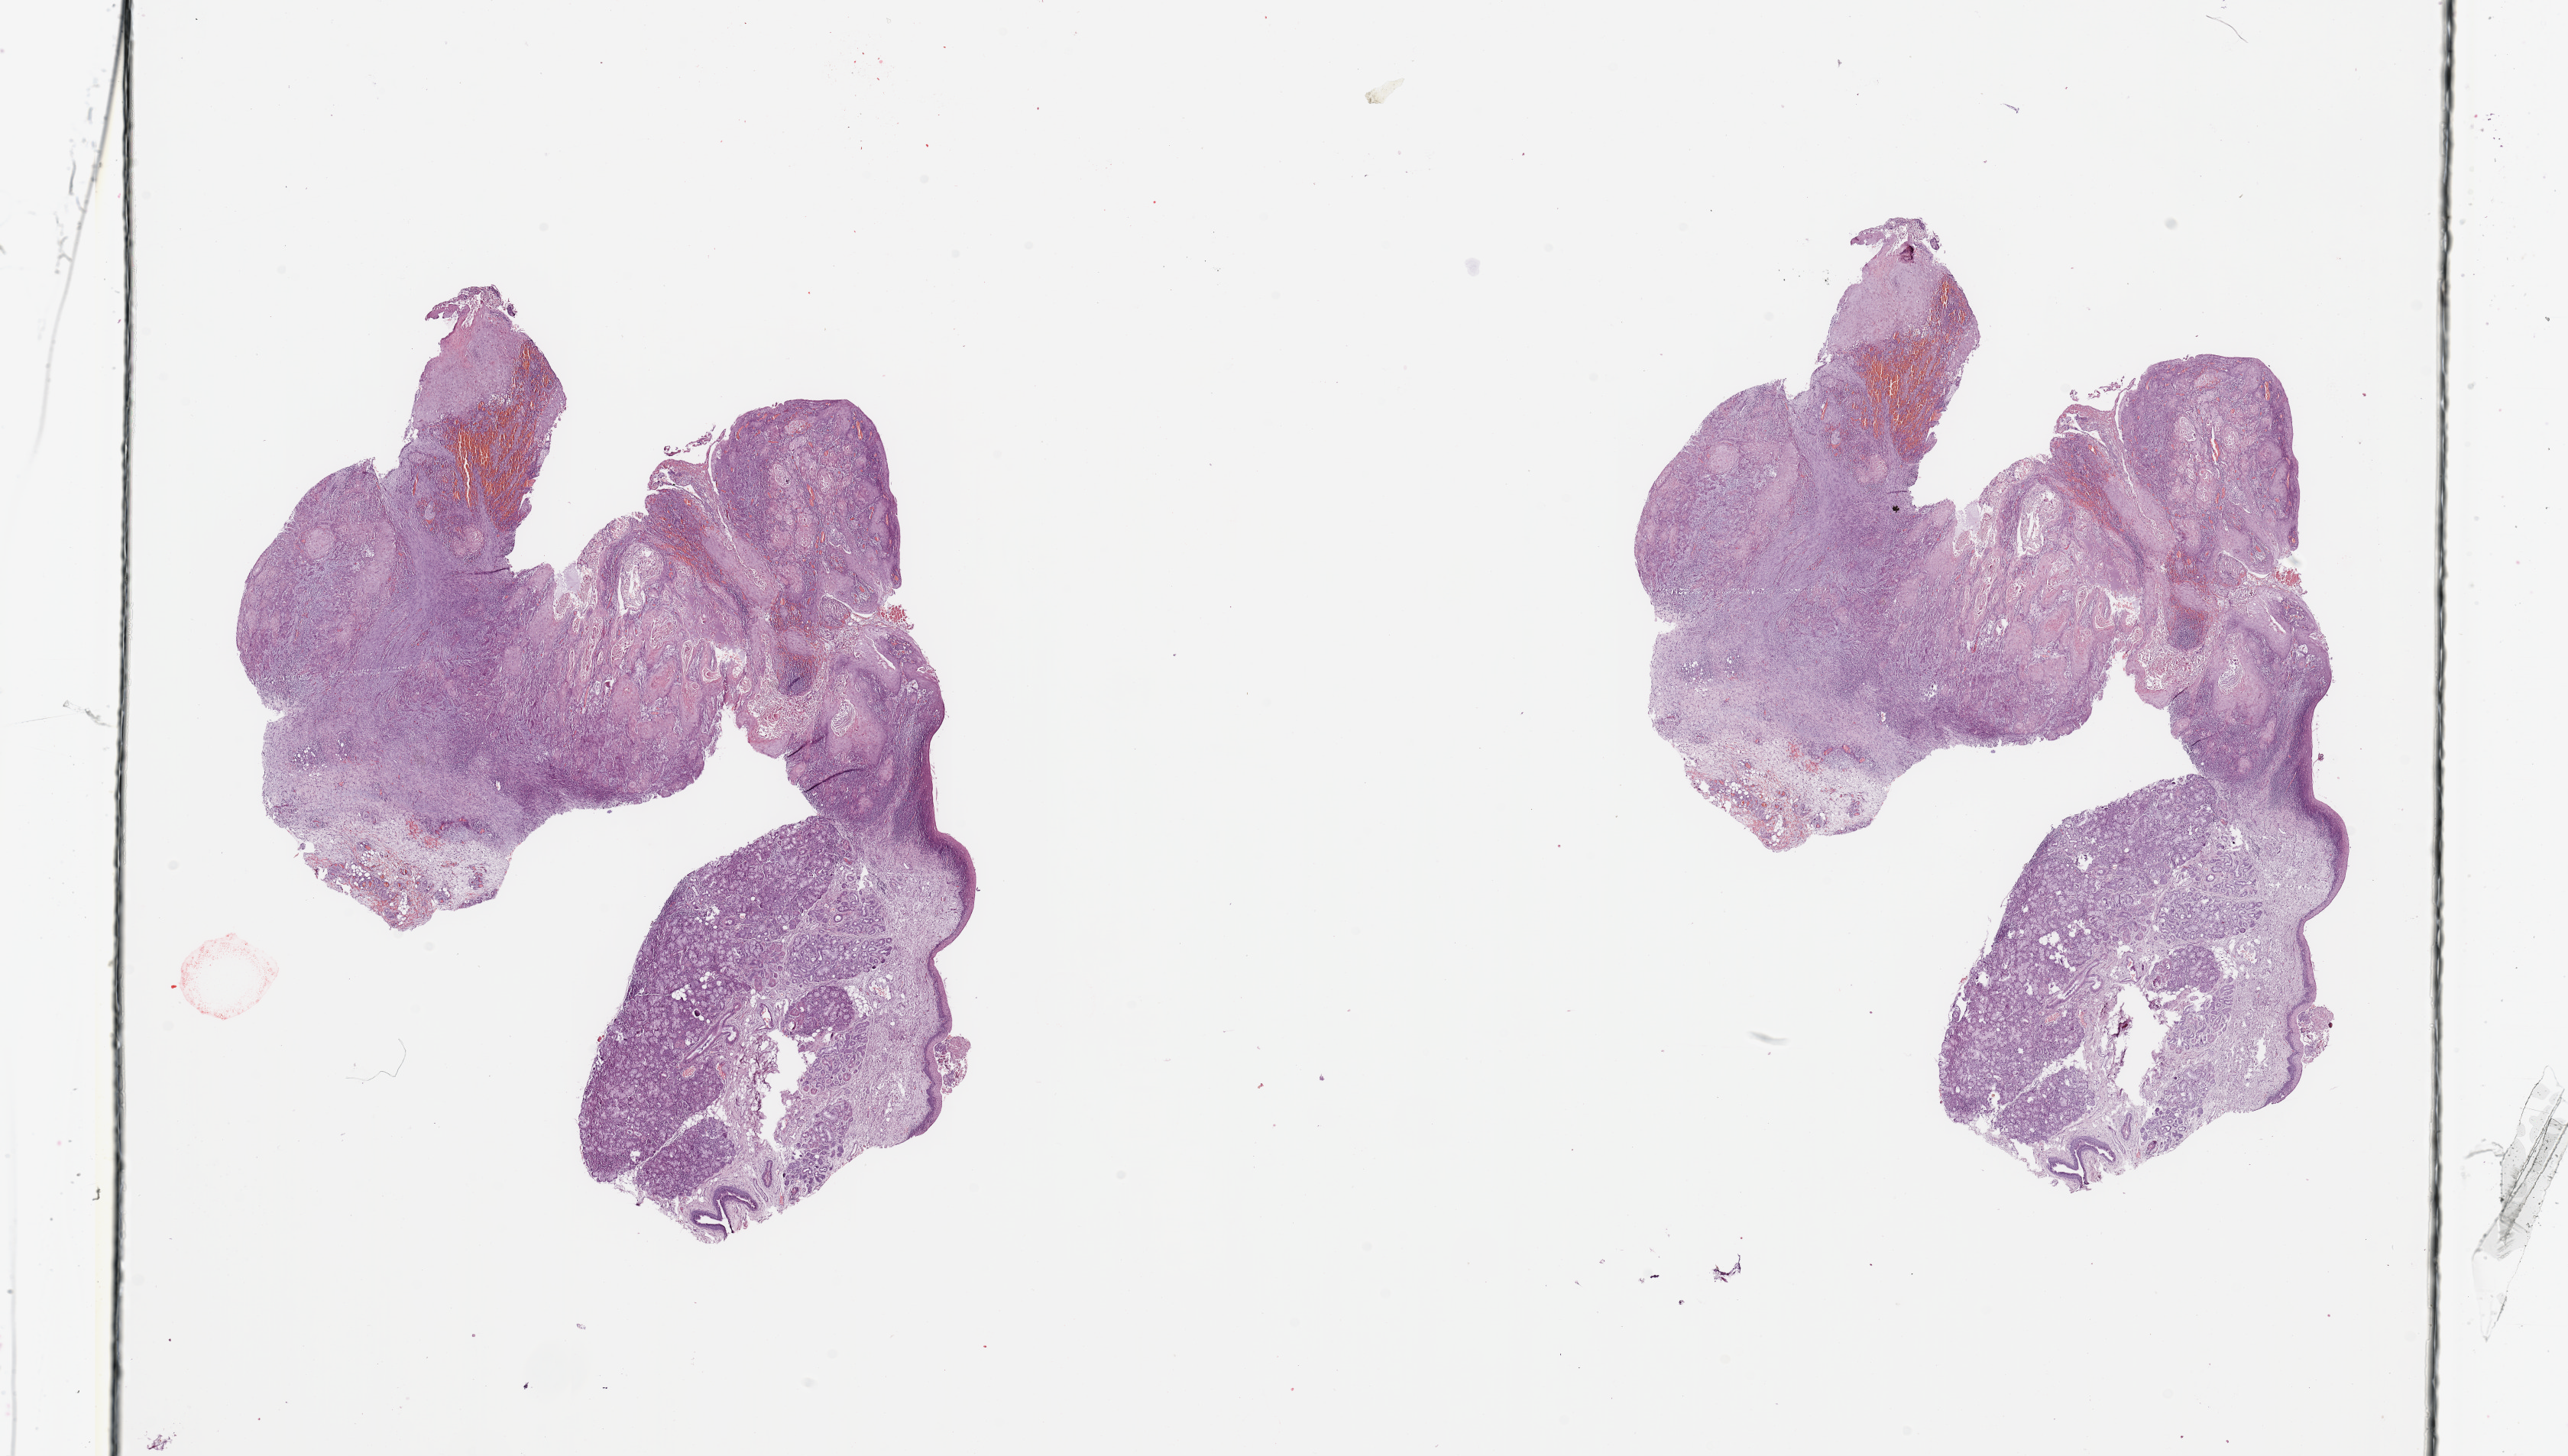
Digitized H&E tissue section (whole slide) — whole scanned area (about 26.6 x 15.1 mm, acquisition: 20x scan) shown as a low-resolution overview, head and neck, tissue type not recorded. Patient: female, age 70 years.
Patient diagnosis: Squamous cell carcinoma, NOS.